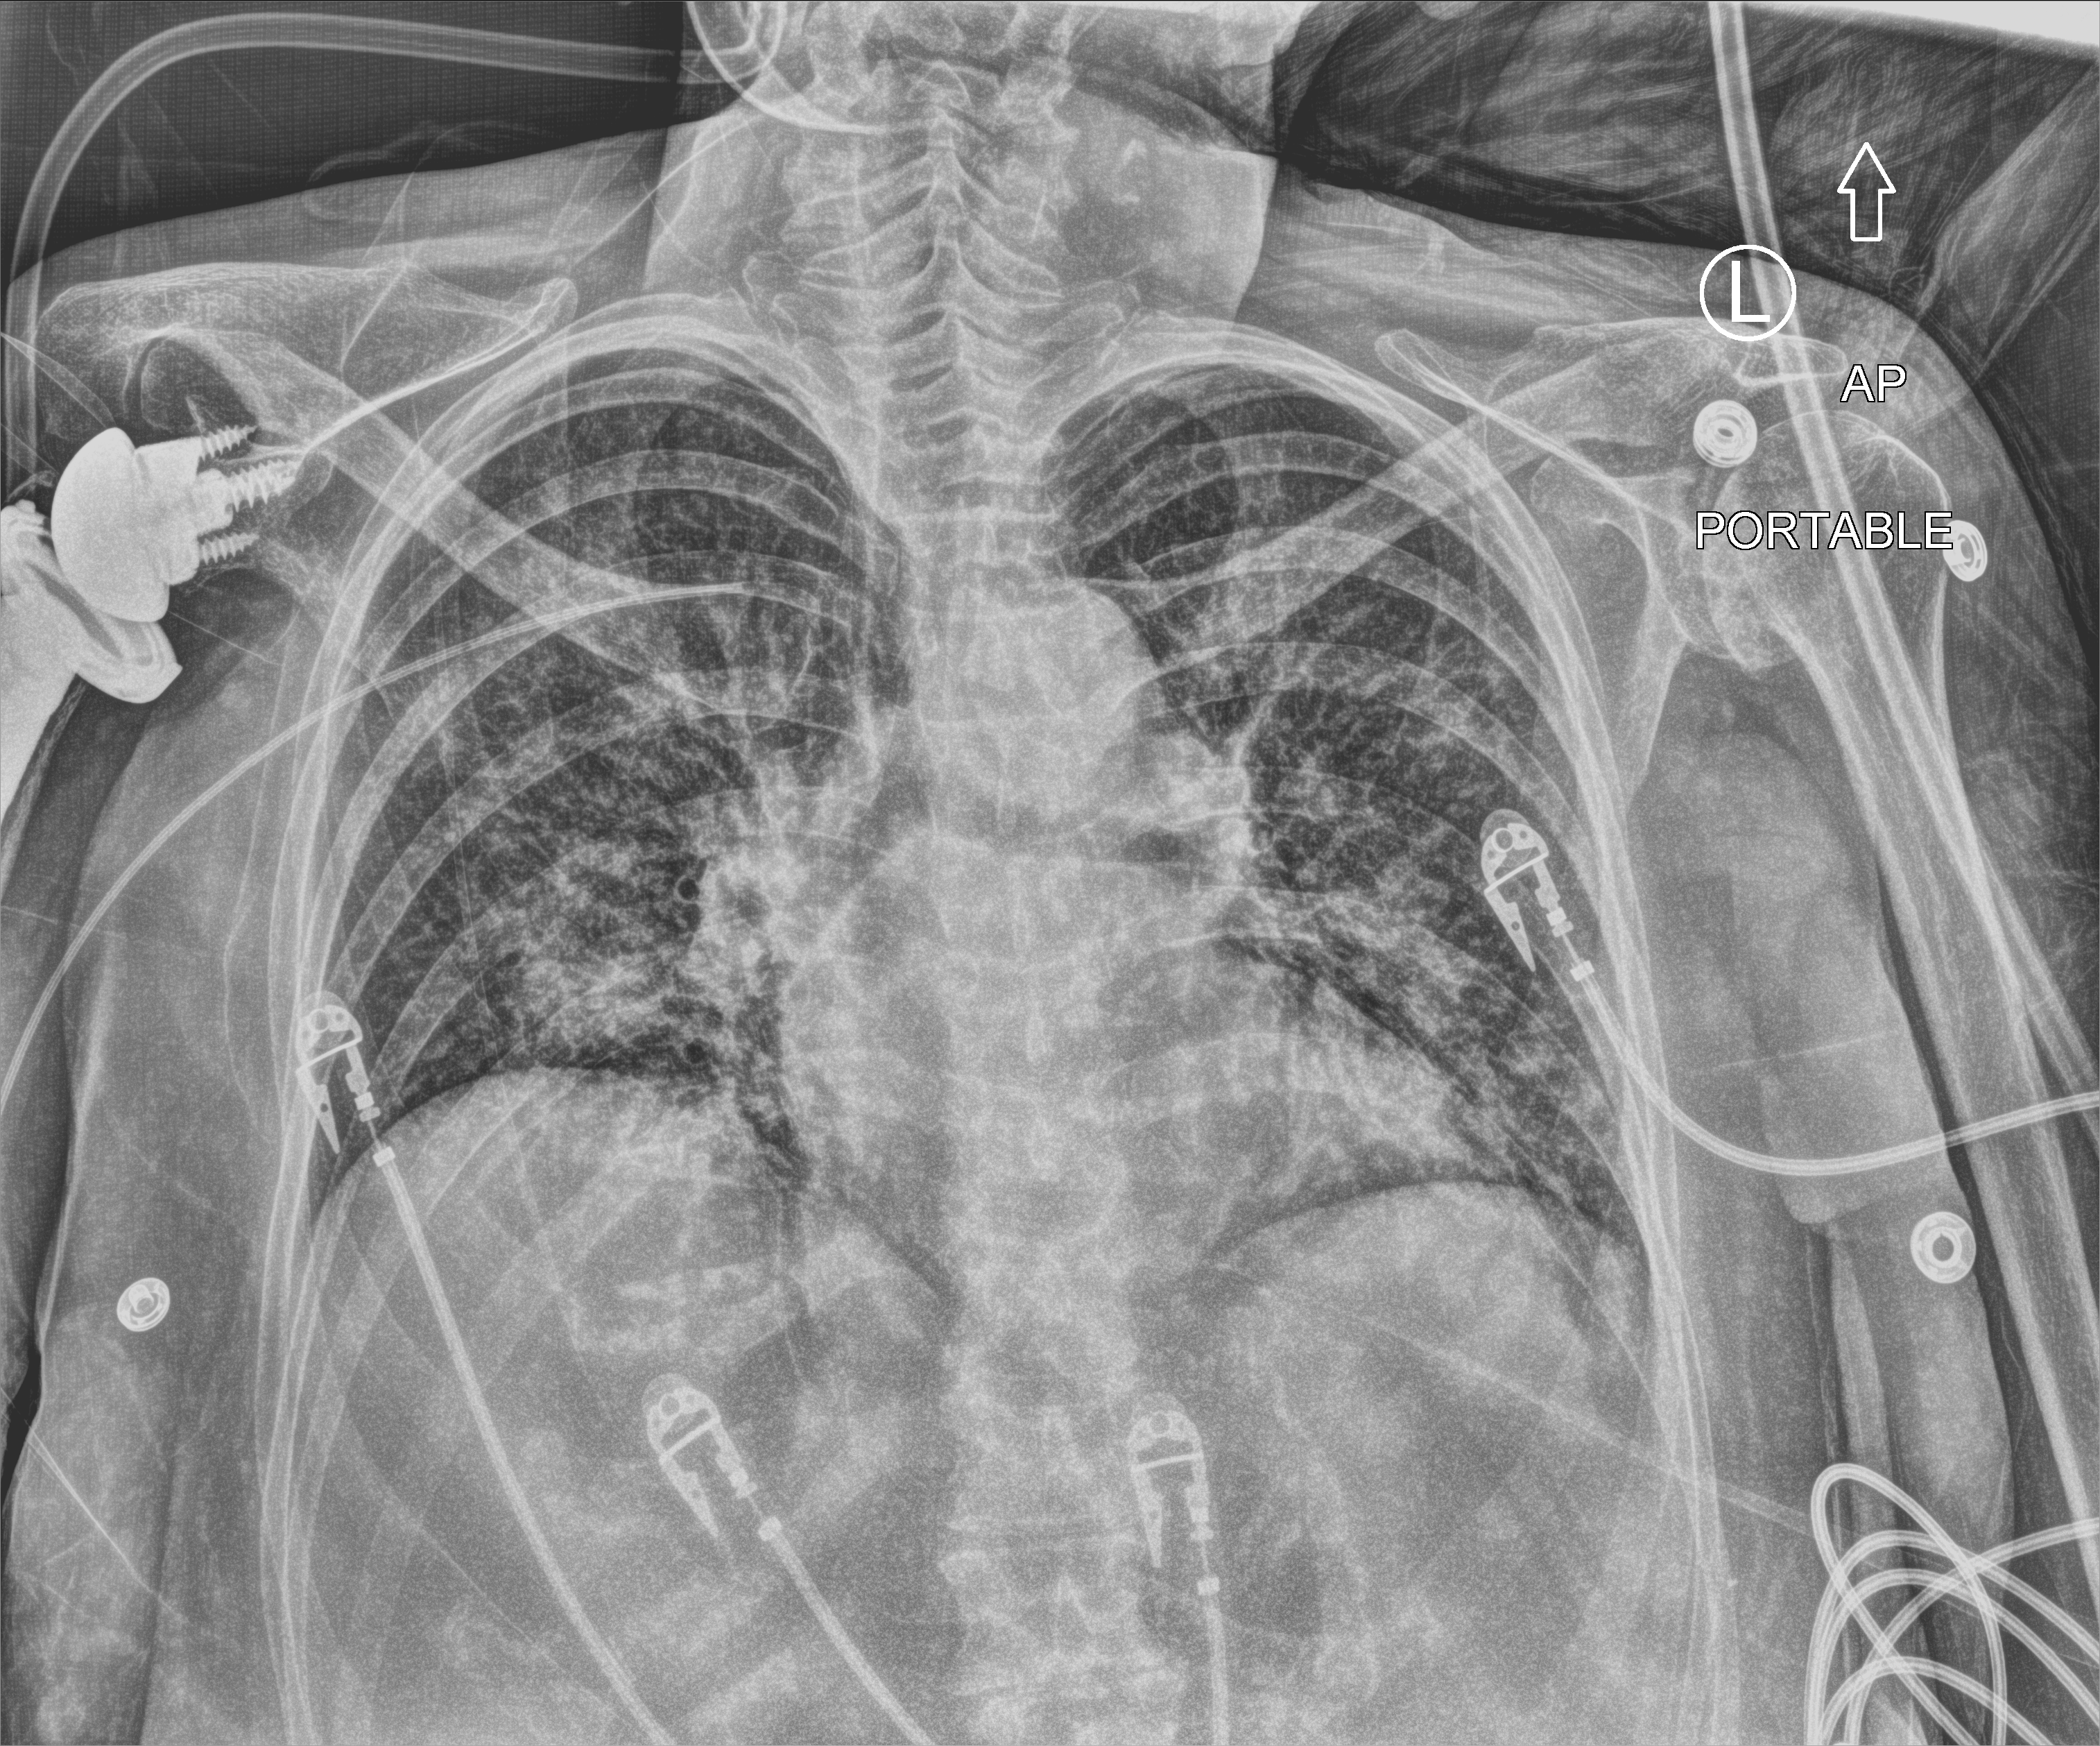
Portable chest radiograph; anteroposterior (AP) projection. Patient hospitalised with COVID-19; female, aged 60–74 years.
Admission-level facts for this patient (not findings on this image; timing relative to this image not recorded): mechanically ventilated during this hospital stay: yes; admitted to intensive care during this hospital stay: yes.